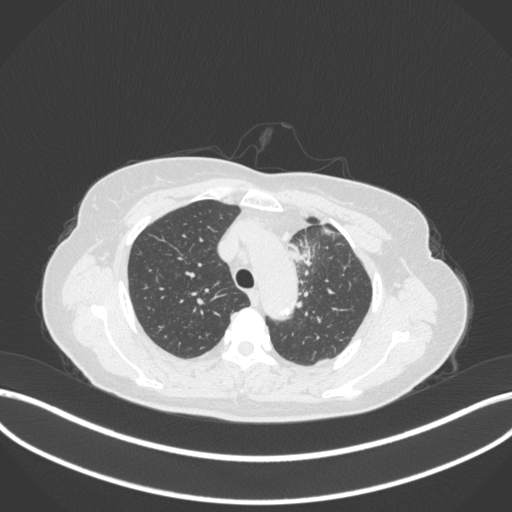
Chest CT, one axial slice; position 256 of 368 along the scan axis; reconstruction kernel B31f; 120 kVp; lung window (W 1500 / L -600 HU); 1 mm slice thickness; 512 × 512 image matrix, field of view 400 × 400 mm. Patient: female, 65 years. Case-level facts recorded for this patient, not image findings: clinical TNM (as recorded): T2a N0 M0; histopathological grade: G2-3.
Structures marked on this image (bounding box drawn by a radiologist):
- lung tumour (recorded histology: adenocarcinoma): bounding box [x1, y1, x2, y2] px = [283, 239, 317, 264]